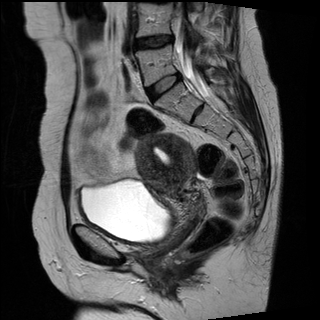
Pelvic MRI for cervical cancer, one sagittal slice. Slice 15 of 27 in the series (ordered by position). T2-weighted. 1.5 T. TE 89 ms, TR 2740 ms. 4 mm slice thickness. 320 × 320 image matrix, field of view 260 × 260 mm. Patient: female, 42 years.
Annotated regions visible in this slice (manually delineated by an expert):
- uterus and cervix: bounding box <137,133,196,200> (left, top, right, bottom; pixels)